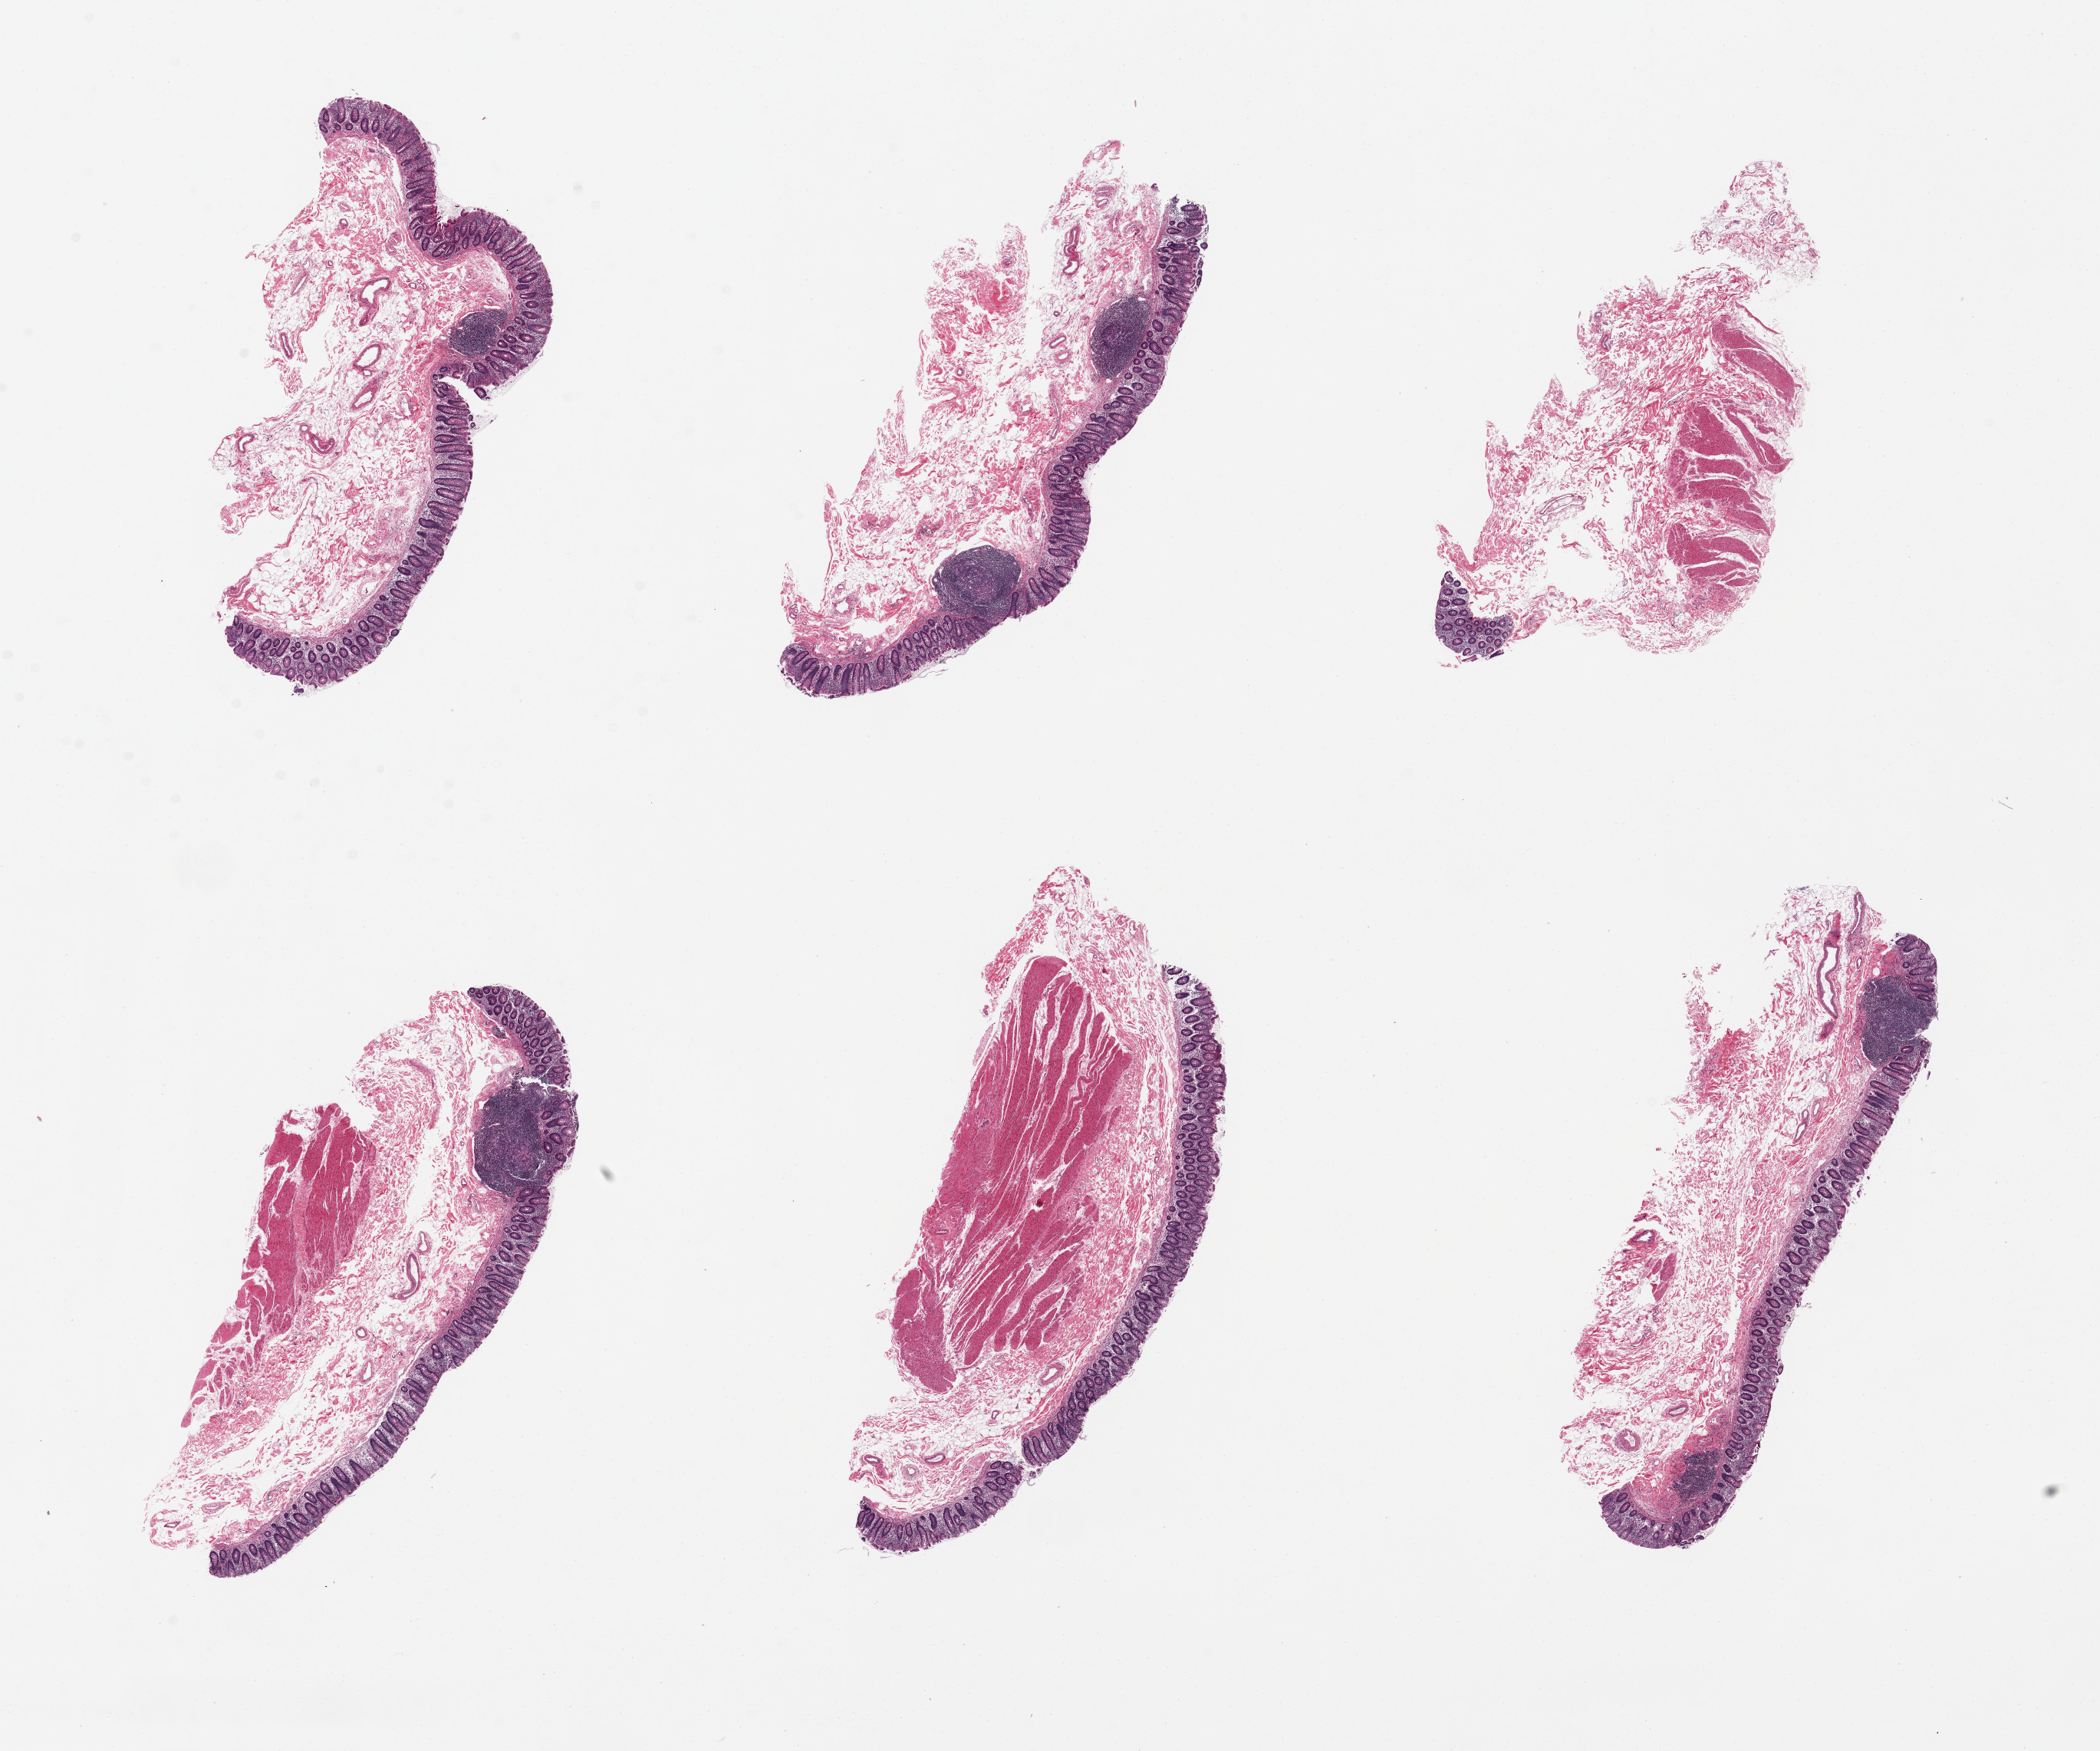
H&E whole-slide image, brightfield — shown as a low-resolution overview of the whole scanned area (about 21.7 x 18.1 mm); PAXgene-fixed paraffin-embedded (PFPE) section; sampled site (target tissue): ileum; donor tissue sample. Male donor.
- pathologist's review note for this sample: 6 pieces, up to 7x3mm; colon in all 6; no ileum